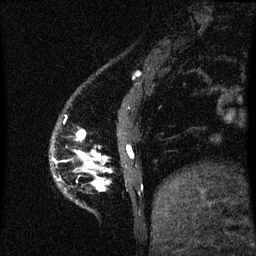
Breast MRI (dynamic contrast-enhanced), one sagittal slice; slice 8 of 60 in the series (ordered by position); dynamic contrast-enhanced series, image 2 of 3 at this slice position (ordered by acquisition); 1.5 T; TE 4.2 ms, TR 8 ms; 2 mm slice thickness; 256 × 256 image matrix, field of view 190 × 190 mm. Female patient, age 50 years.
Annotated regions visible in this slice (semi-automatic segmentation, software-assisted and operator-edited):
- analysis volume of interest (the breast-tissue region the enhancement analysis was run in; not a lesion): box from (x=74, y=130) to (x=99, y=186) px
- tumour enhancement mask (voxels above the 70 % enhancement threshold inside the analysis volume of interest): (x=79, y=135)–(x=83, y=138)